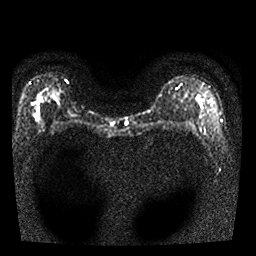
Breast MRI, one axial slice; diffusion-weighted series; image 2 of 4 stored at this slice position (different b-values; order by instance number); 1.5 T; 256 × 256 image matrix. Female patient.
Annotated regions visible in this slice (manually delineated by an expert):
- tumour on diffusion-weighted imaging: box from (x=34, y=103) to (x=42, y=122) px